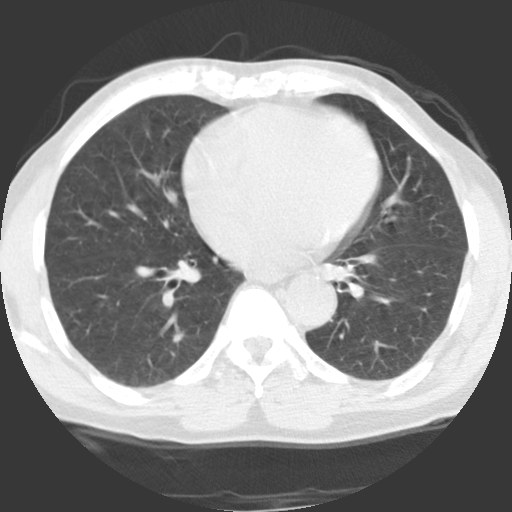
Chest CT (low-dose screening protocol), one axial image, baseline annual screen, lung window (W 1500 / L -600 HU), 2.5 mm slice thickness, standard (soft-tissue) reconstruction kernel (STANDARD), 140 kVp, slice 39 of 109 in the series, 512 × 512 image matrix, field of view 288 × 288 mm. Male participant, aged 58 years at enrolment. Current smoker at enrolment.
Expert-annotated lung lesion, bounding box <159,324,193,352> (left, top, right, bottom; pixels). Screening reader's record for this exam (one nodule recorded; not confirmed to be the boxed lesion): non-calcified nodule or mass ≥4 mm, left upper lobe, 10 × 9 mm, poorly defined margins, ground glass attenuation. Note: the box lies in the patient's right hemithorax on this image, whereas the reader's record names the left lung; they may be different findings.